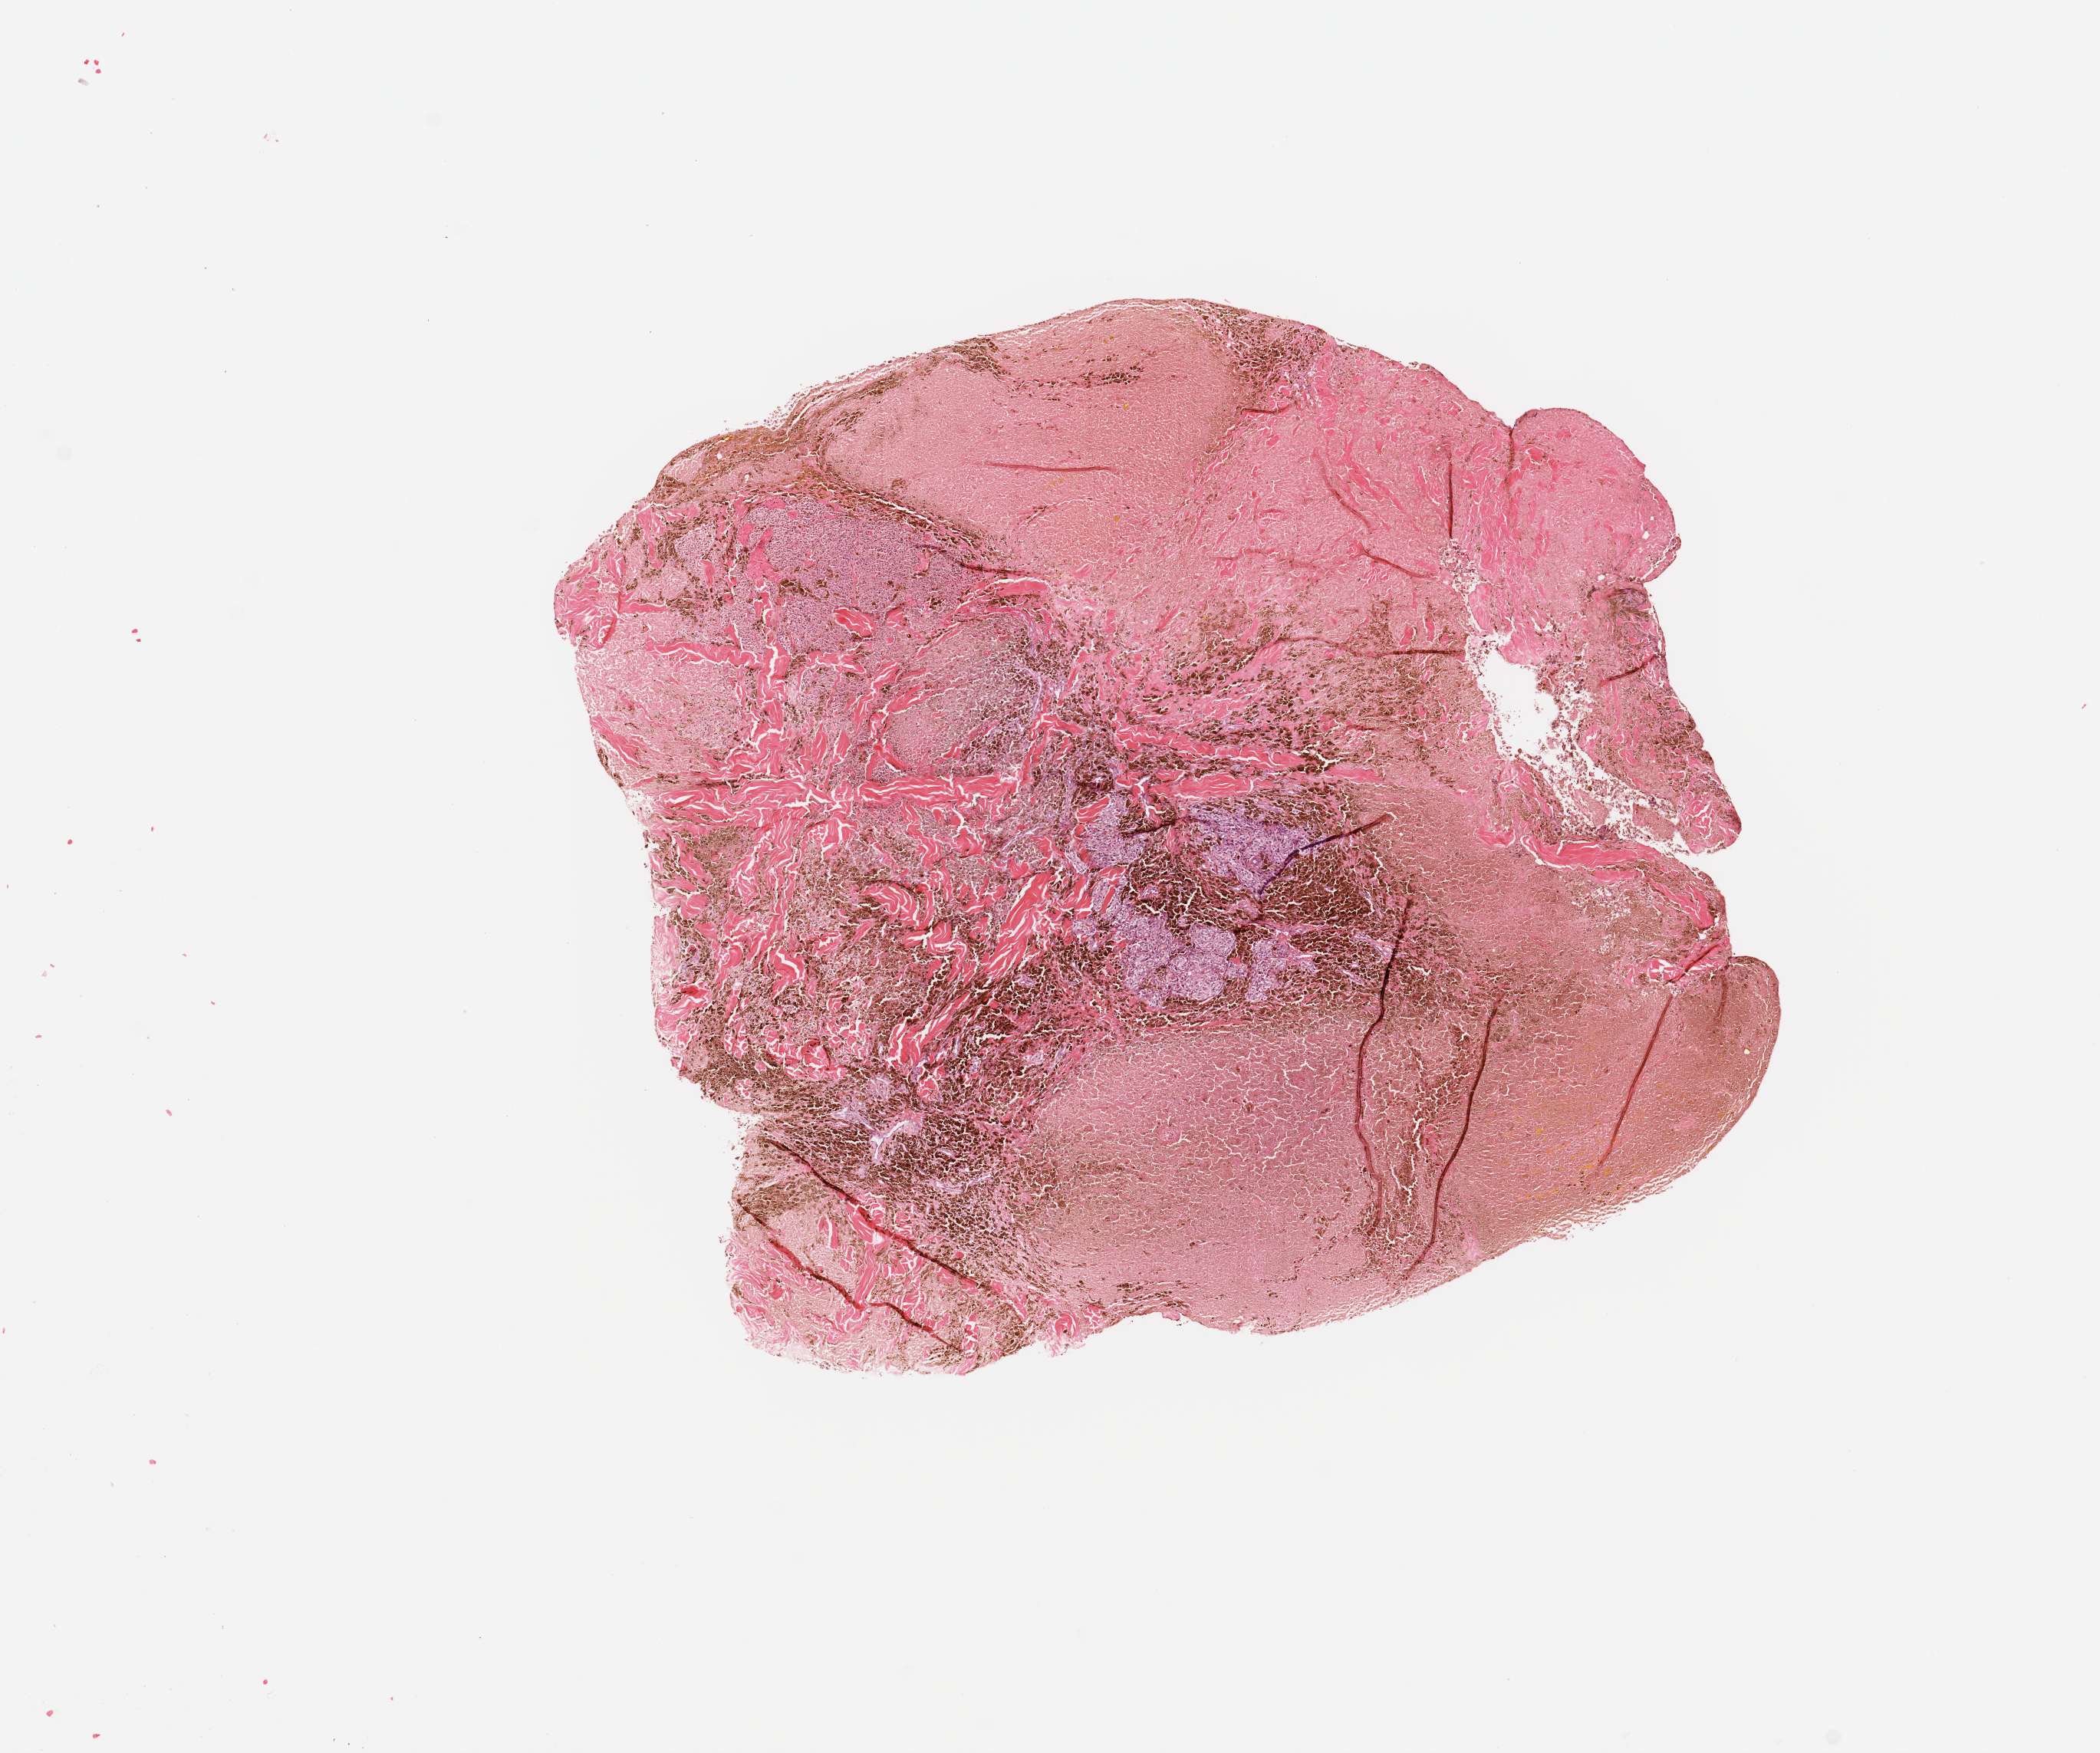
Whole-slide histology image, H&E — low-resolution overview of the scanned area, about 10.8 x 9.0 mm. Melanoma tumour tissue; sampled site not recorded. 81-year-old female patient.
Histologic diagnosis: Malignant melanoma, NOS. AJCC pathologic stage: IIC. Primary tumour site (as recorded): trunk.